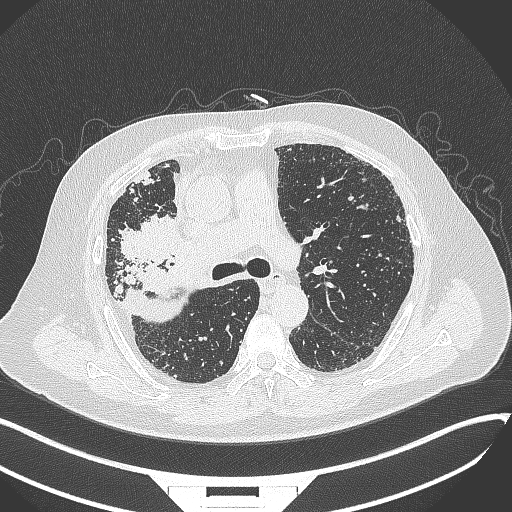
Chest CT, one axial slice; position 218 of 384 along the scan axis; lung window (W 1500 / L -600 HU); 1 mm slice thickness; 512 × 512 image matrix, field of view 400 × 400 mm. Patient: male, 69 years. Case-level facts recorded for this patient, not image findings: clinical TNM (as recorded): T4 N3 M1.
Annotated regions visible in this slice (rectangle marked by the reading radiologist):
- lung tumour (recorded histology: adenocarcinoma): box from (x=115, y=207) to (x=187, y=273) px